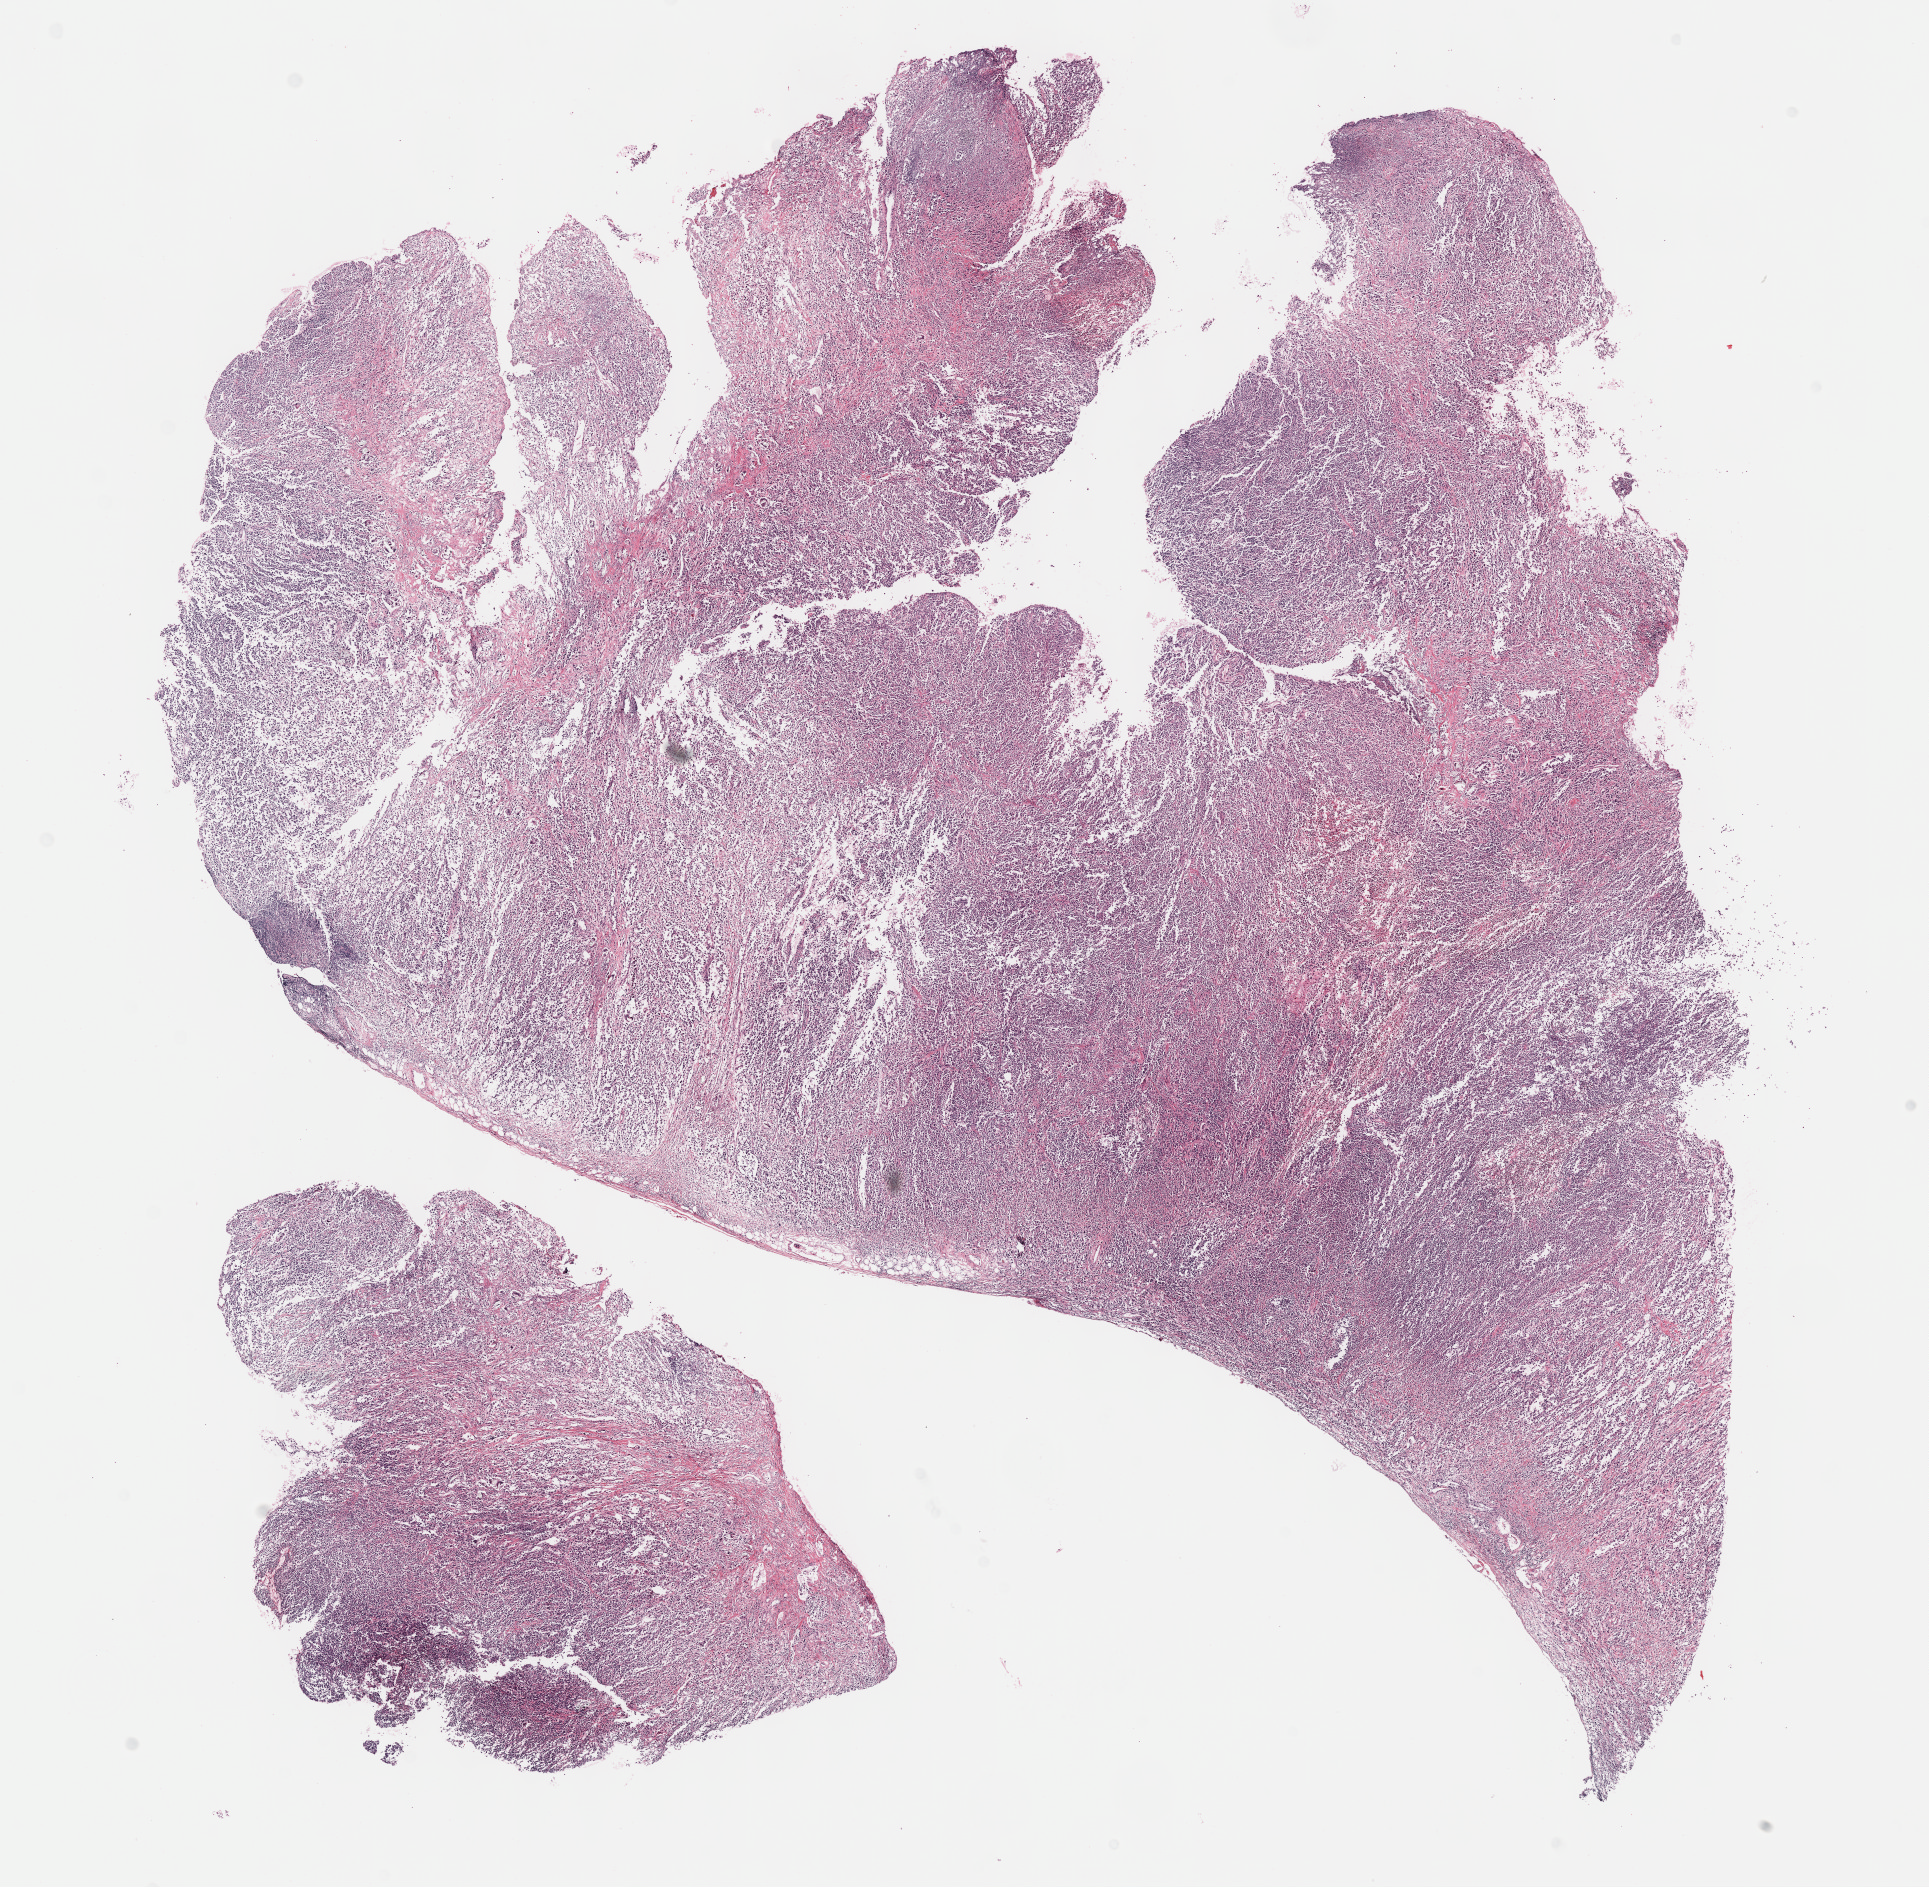
Digitized H&E tissue section (whole slide), whole scanned area (about 15.6 x 15.3 mm) shown as a low-resolution overview. FFPE section. Sample: primary tumour, lung. Male, age 71 years at initial diagnosis.
- AJCC pathologic stage: IIIA
- pathologic diagnosis: Adenocarcinoma, NOS